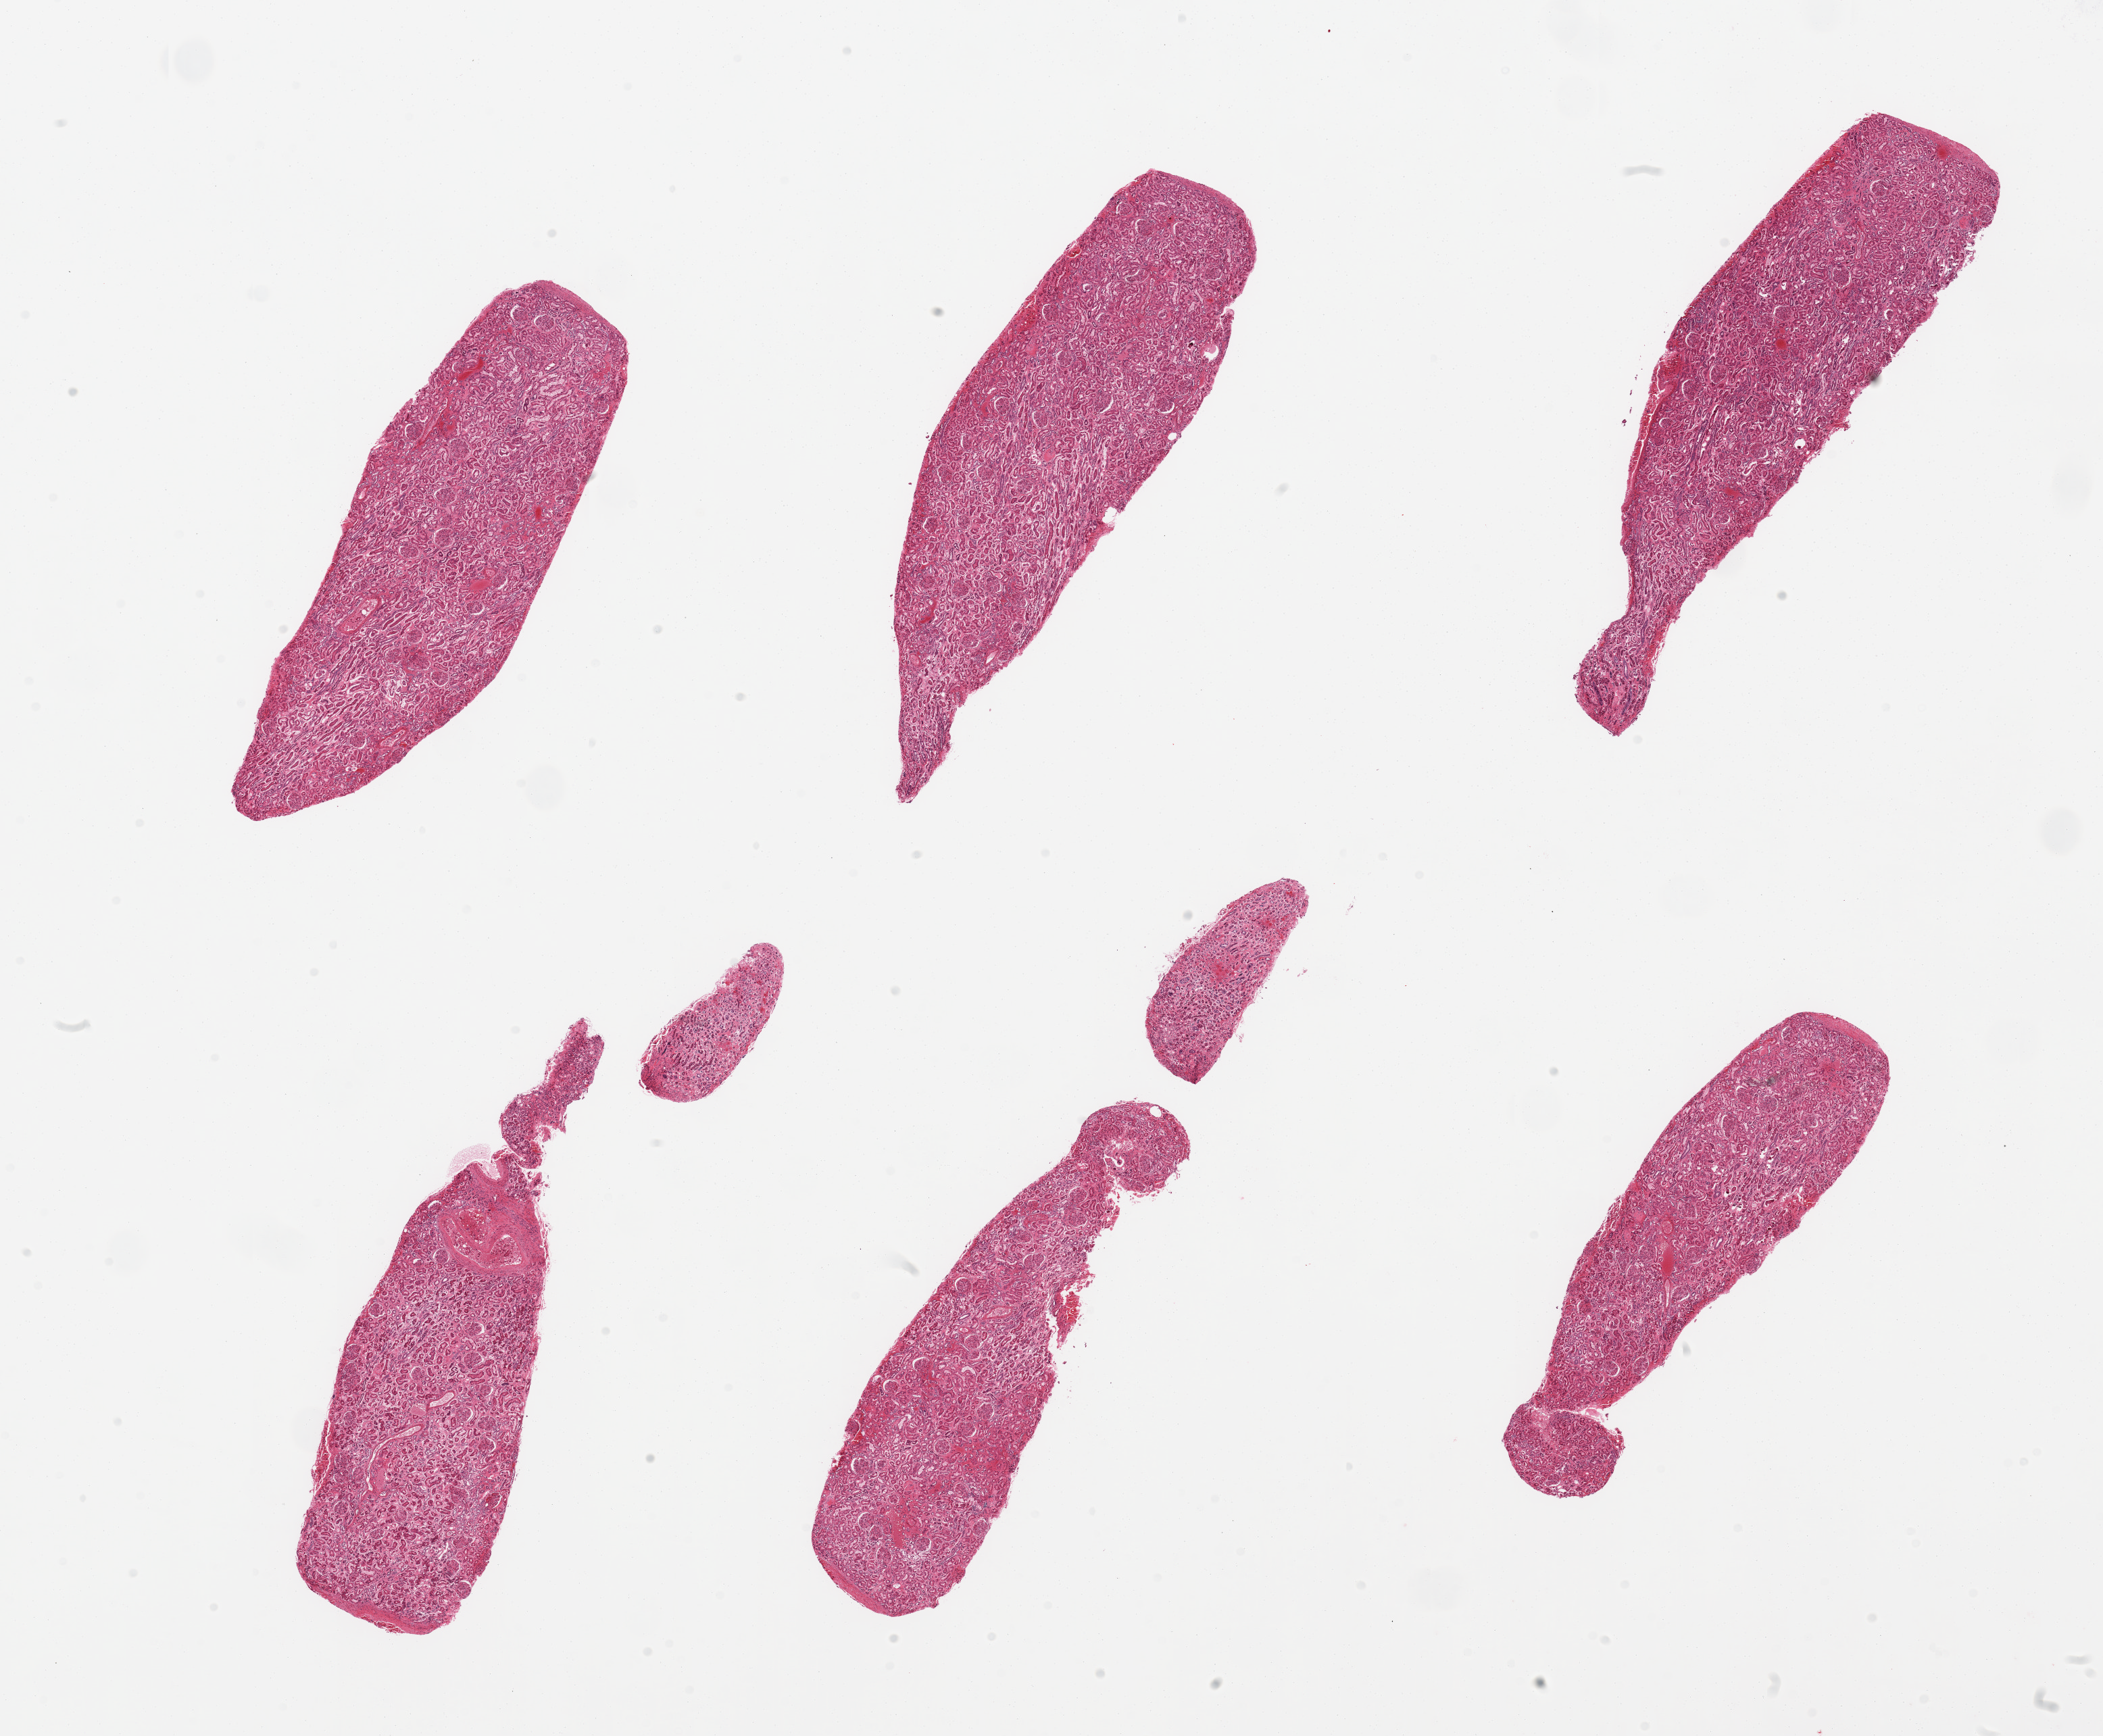
Haematoxylin and eosin whole-slide image — low-resolution overview of the scanned area, about 24.6 x 20.3 mm; PAXgene-fixed paraffin-embedded (PFPE) section; section of renal cortex (target tissue); tissue donor sample. Donor sex: female.
- reviewer comment on this tissue sample: 6 pieces + some fragments